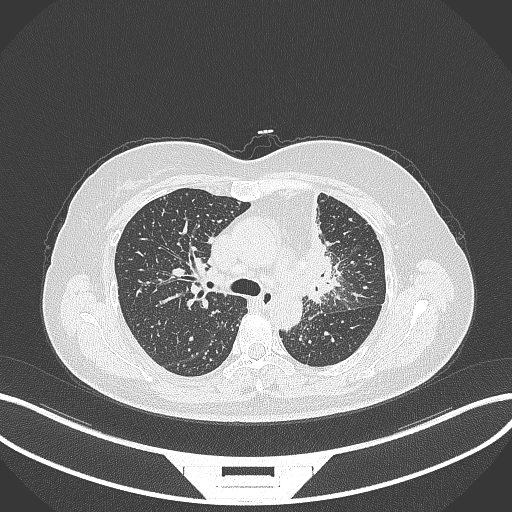
Chest CT, one axial slice. Position 223 of 348 along the scan axis. Reconstruction kernel B70f. 120 kVp. Lung window (W 1500 / L -600 HU). 1 mm slice thickness. 512 × 512 image matrix, field of view 400 × 400 mm. Patient: female, 49 years. From the clinical record (not read from this slice): clinical TNM (as recorded): T1c N0 M1.
Structures marked on this image (rectangle marked by the reading radiologist):
- lung tumour (recorded histology: adenocarcinoma): bounding box <292,189,344,309> (left, top, right, bottom; pixels)